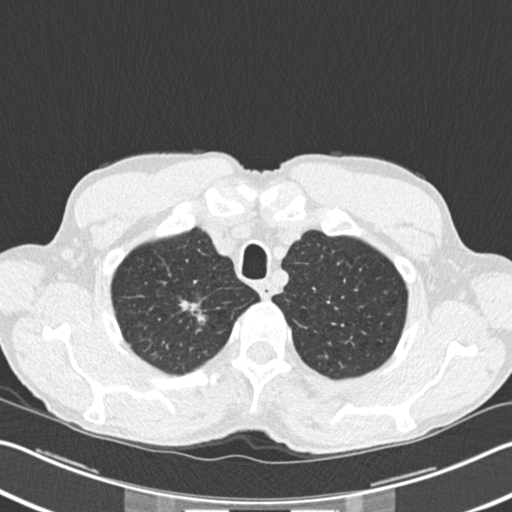
Chest CT (low-dose screening protocol), one axial image; second annual screen; lung window (W 1500 / L -600 HU); 2 mm slice thickness; standard (soft-tissue) reconstruction kernel (B30f); 120 kVp; slice 30 of 220 in the series; 512 × 512 image matrix, field of view 342 × 342 mm. Male participant, aged 62 years at enrolment. Former smoker at enrolment.
Expert-annotated lung lesion, box from (x=172, y=291) to (x=213, y=338) px. The screening reader recorded 2 non-calcified nodules or masses ≥4 mm on this exam (right upper lobe, right upper lobe); which of them this box marks is not recorded. Later outcome: lung cancer diagnosed 5 days after this screen — bronchiolo-alveolar adenocarcinoma, NOS, right upper lobe, well differentiated (G1), stage IA (AJCC 6th edition), 15 mm at pathology.